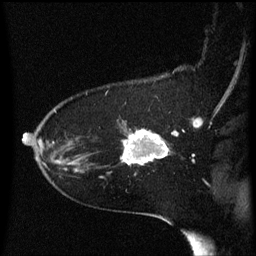
Breast MRI (dynamic contrast-enhanced), one sagittal slice; position 43 of 60 along the scan axis; dynamic contrast-enhanced series, image 2 of 3 at this slice position (ordered by acquisition); 1.5 T; TE 4.2 ms, TR 8.4 ms; 256 × 256 image matrix, field of view 200 × 200 mm. Patient: female, 54 years. Case-level facts recorded for this patient, not image findings: setting: breast cancer imaged before/during neoadjuvant chemotherapy; receptor status: HR-positive, HER2-negative.
Outlined on this slice (semi-automatic segmentation, software-assisted and operator-edited):
- analysis volume of interest (the breast-tissue region the enhancement analysis was run in; not a lesion): bounding box [x1, y1, x2, y2] px = [123, 128, 170, 165]
- tumour enhancement mask (voxels above the 70 % enhancement threshold inside the analysis volume of interest): [124, 130, 170, 165]